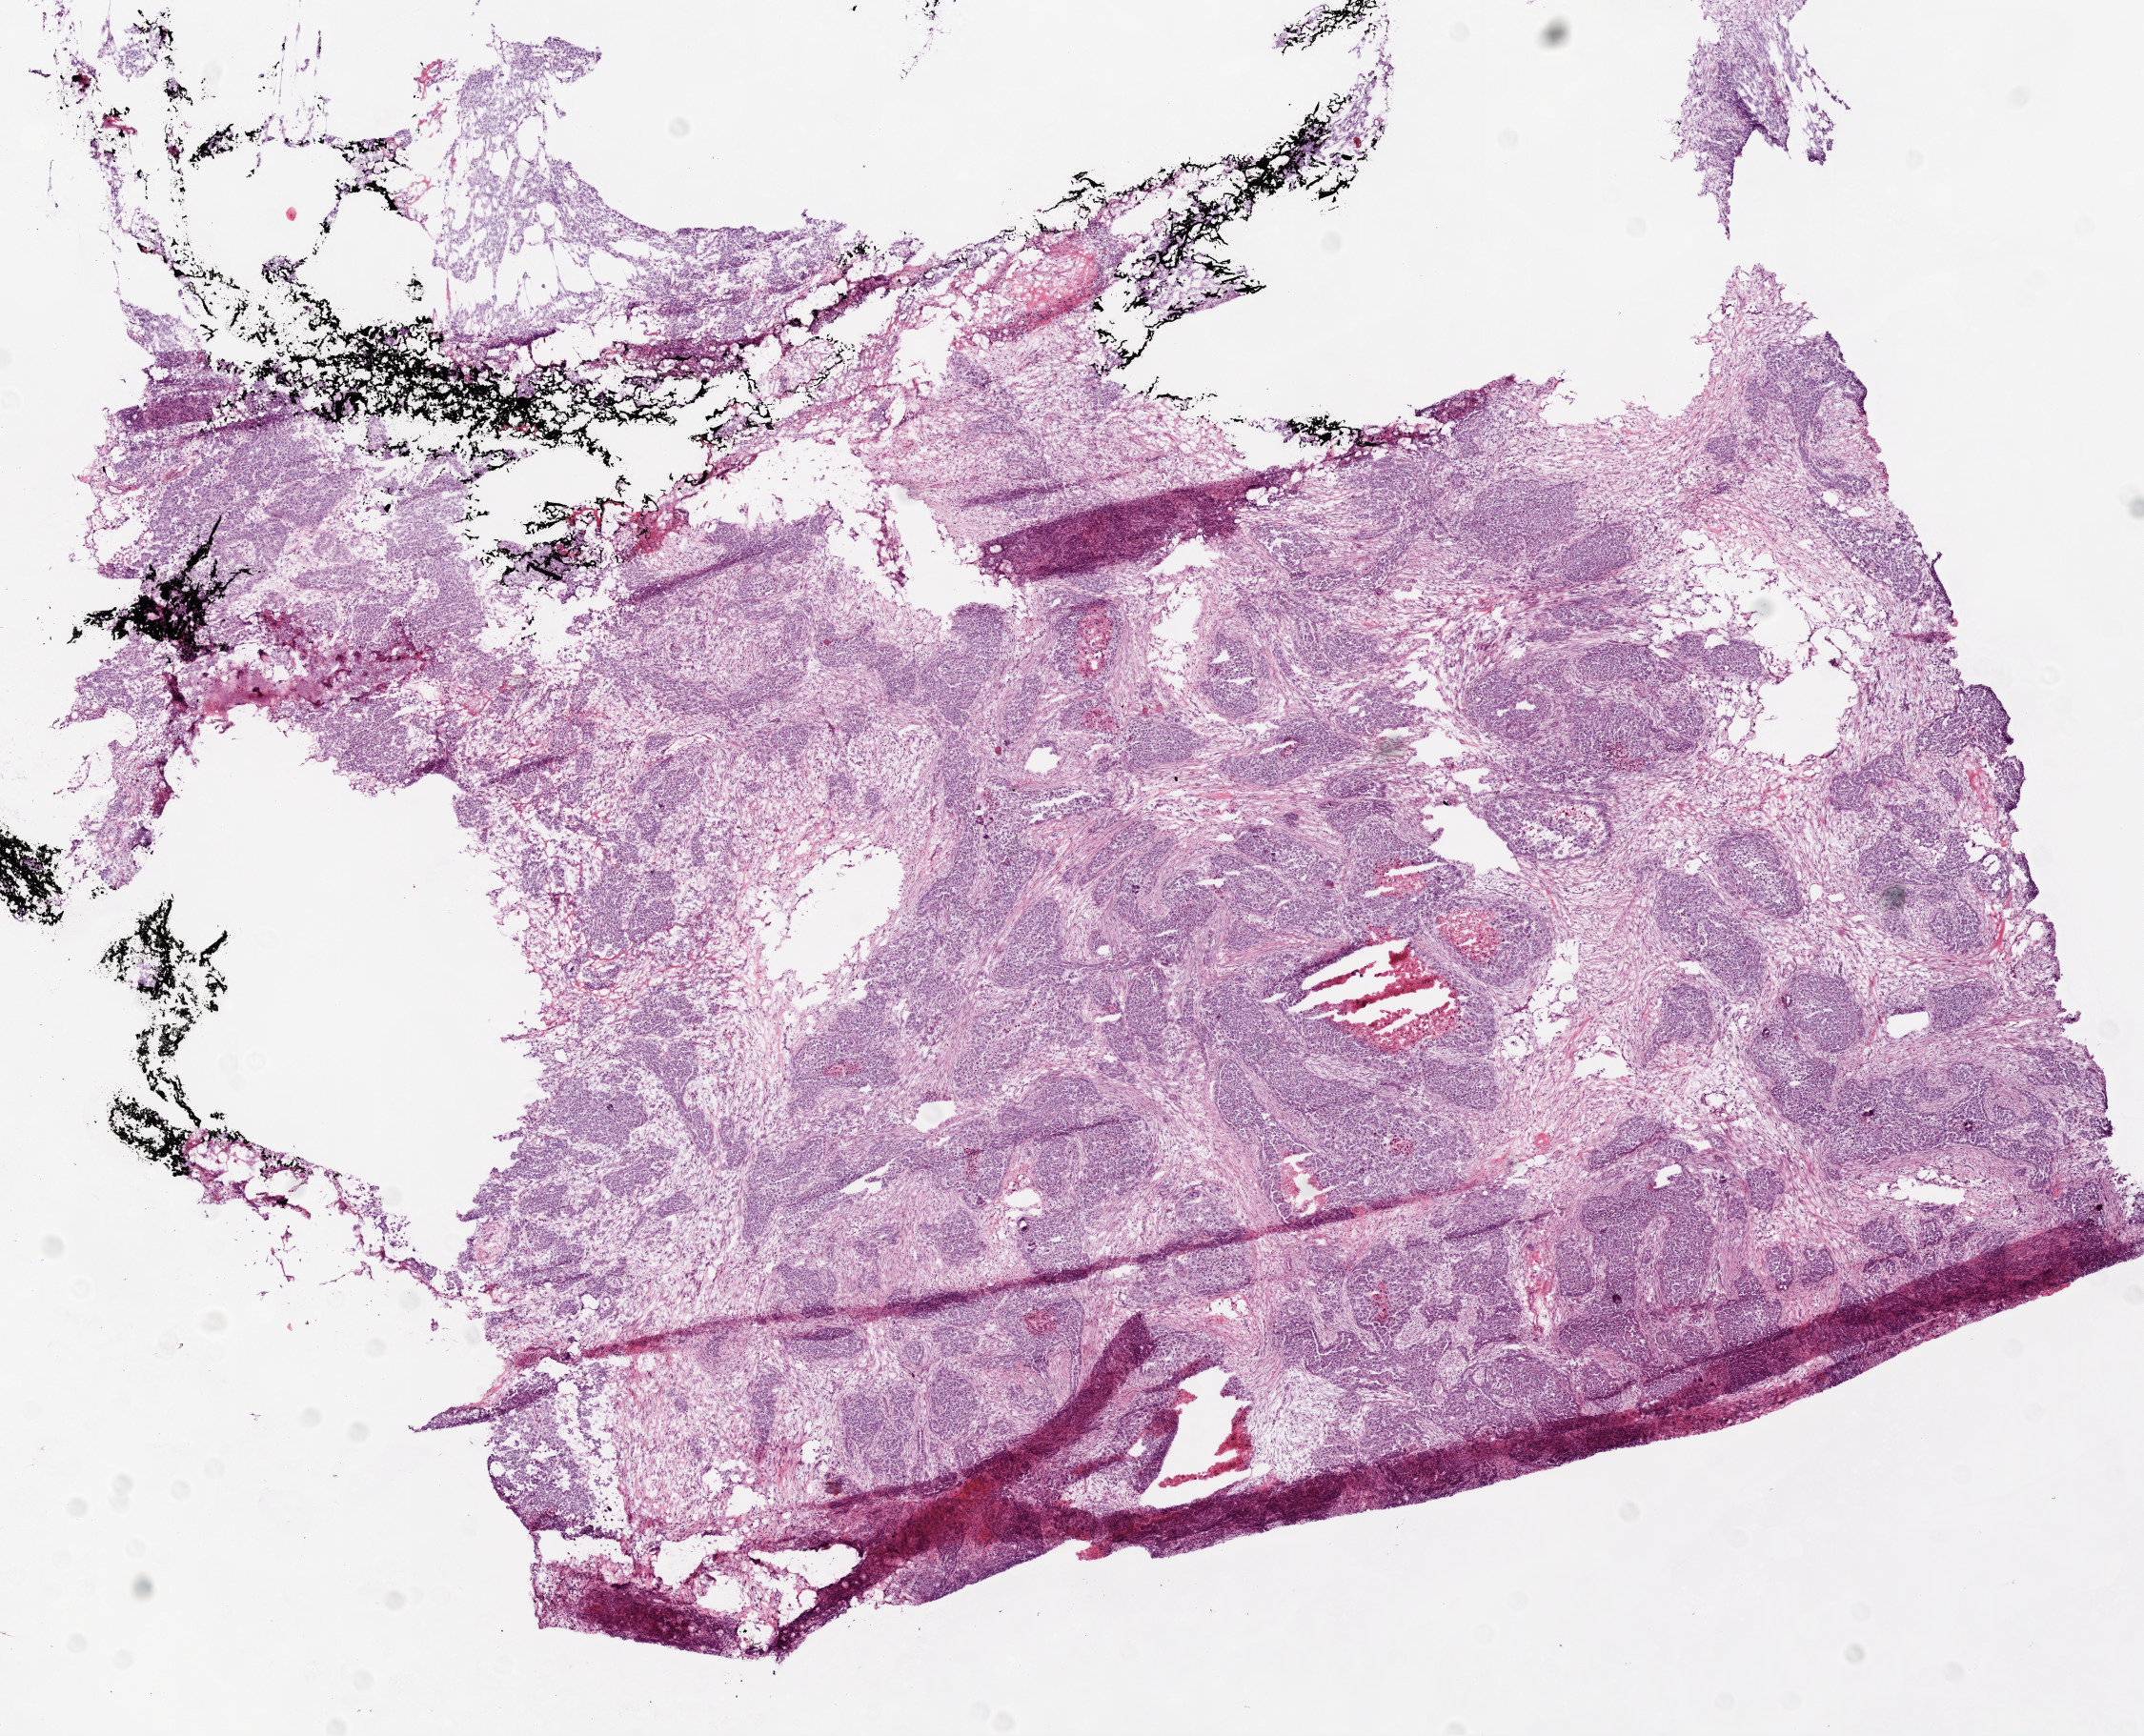
Whole-slide histology image, Hematoxylin and eosin (H&E) stained — shown as a low-resolution overview of the whole scanned area (about 9.0 x 7.3 mm), frozen section, ovary, primary tumour sample. Female, age 57 years at initial diagnosis. Histologic grade: G3 (poorly differentiated). Pathologist review of this section (percent, as recorded): tumour cells 85%, tumour nuclei 90%, normal cells 0%, stromal cells 10%, necrosis 5%.
FIGO stage: IIIC. Histologic diagnosis: Serous cystadenocarcinoma, NOS. Laterality: bilateral.